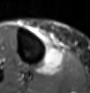
MRI of an extremity soft-tissue mass, one axial slice. Slice 30 of 60 in the series (ordered by position). STIR. MR volume resampled by the dataset authors to the PET/CT grid (not the native acquisition matrix). 90 × 93 image matrix, field of view 88 × 91 mm. Female patient. From the clinical record (not read from this slice): histological type: undifferentiated – high grade; grade: high; site of the primary tumour: right thigh.
Annotated regions visible in this slice (expert contour drawn on MRI and transferred to this co-registered scan by the dataset authors):
- gross tumour volume (mass): bounding box (x1, y1, x2, y2) in pixels: (35, 37, 65, 75)